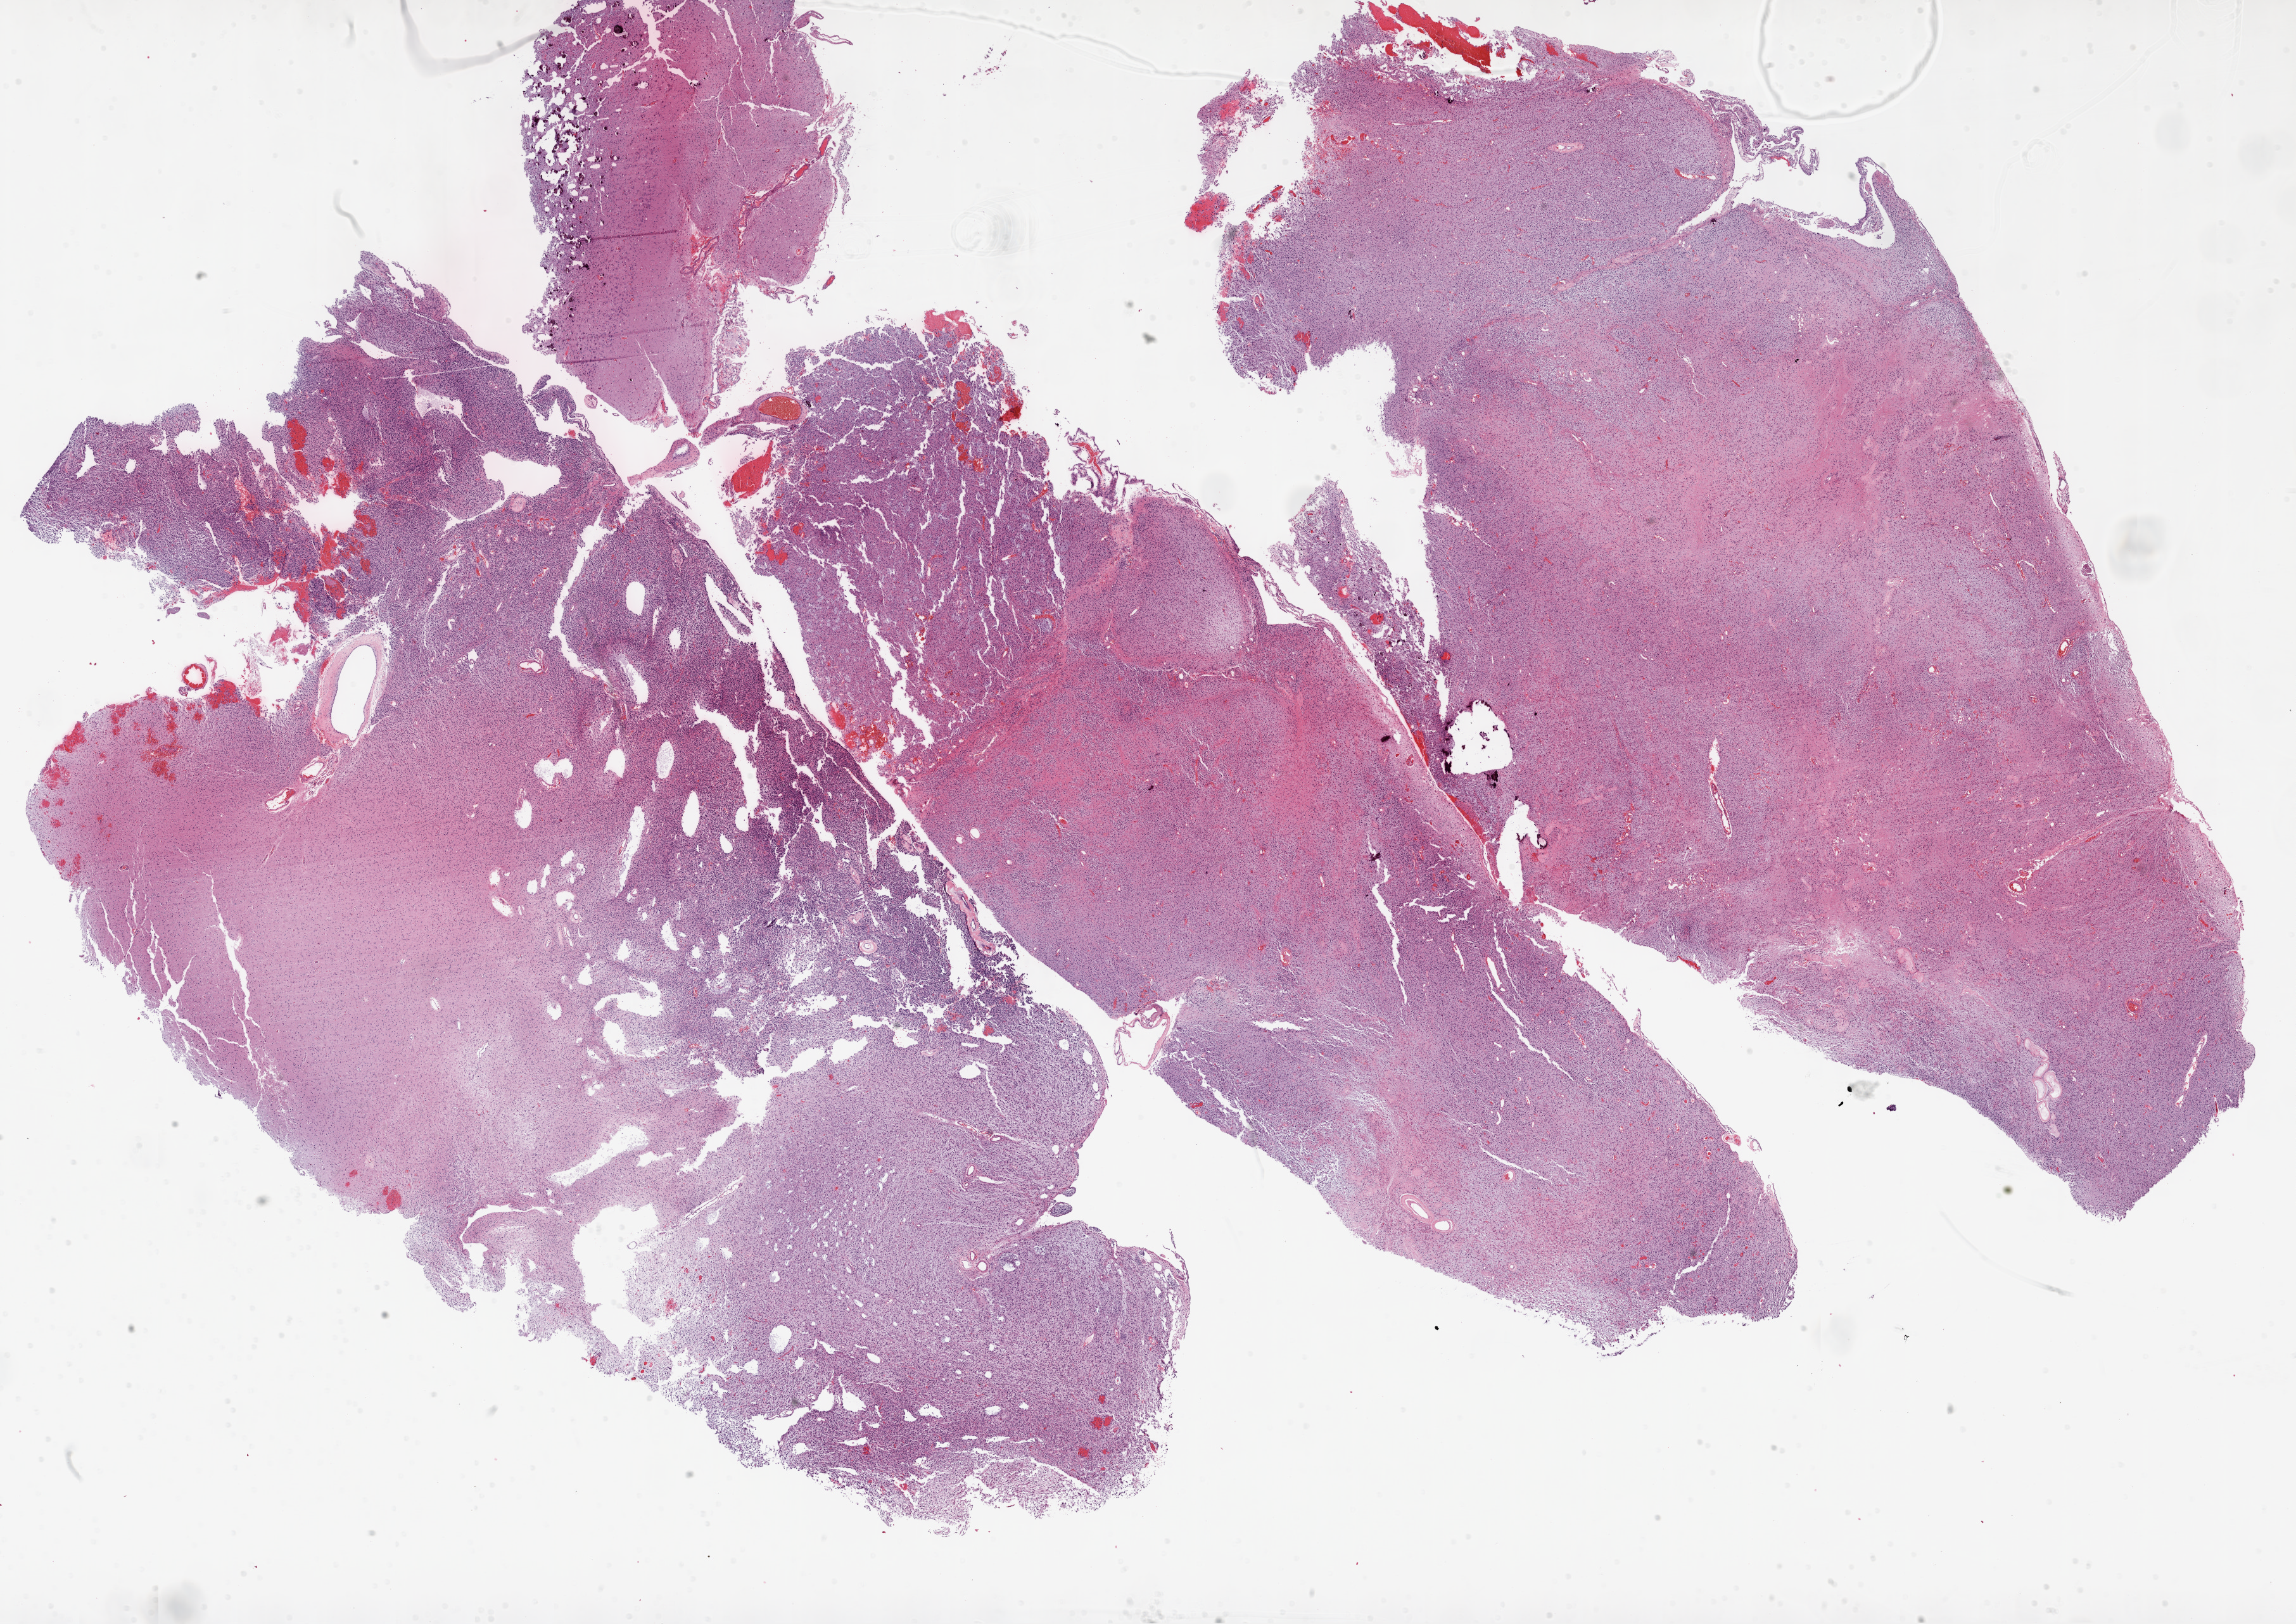
Whole-slide histology image, Hematoxylin and eosin (H&E) stained — shown as a low-resolution overview of the whole scanned area (about 29.1 x 20.6 mm); FFPE section; primary tumour sample from the brain. Male patient; age at initial diagnosis 54 years.
Pathologic diagnosis: Glioblastoma.